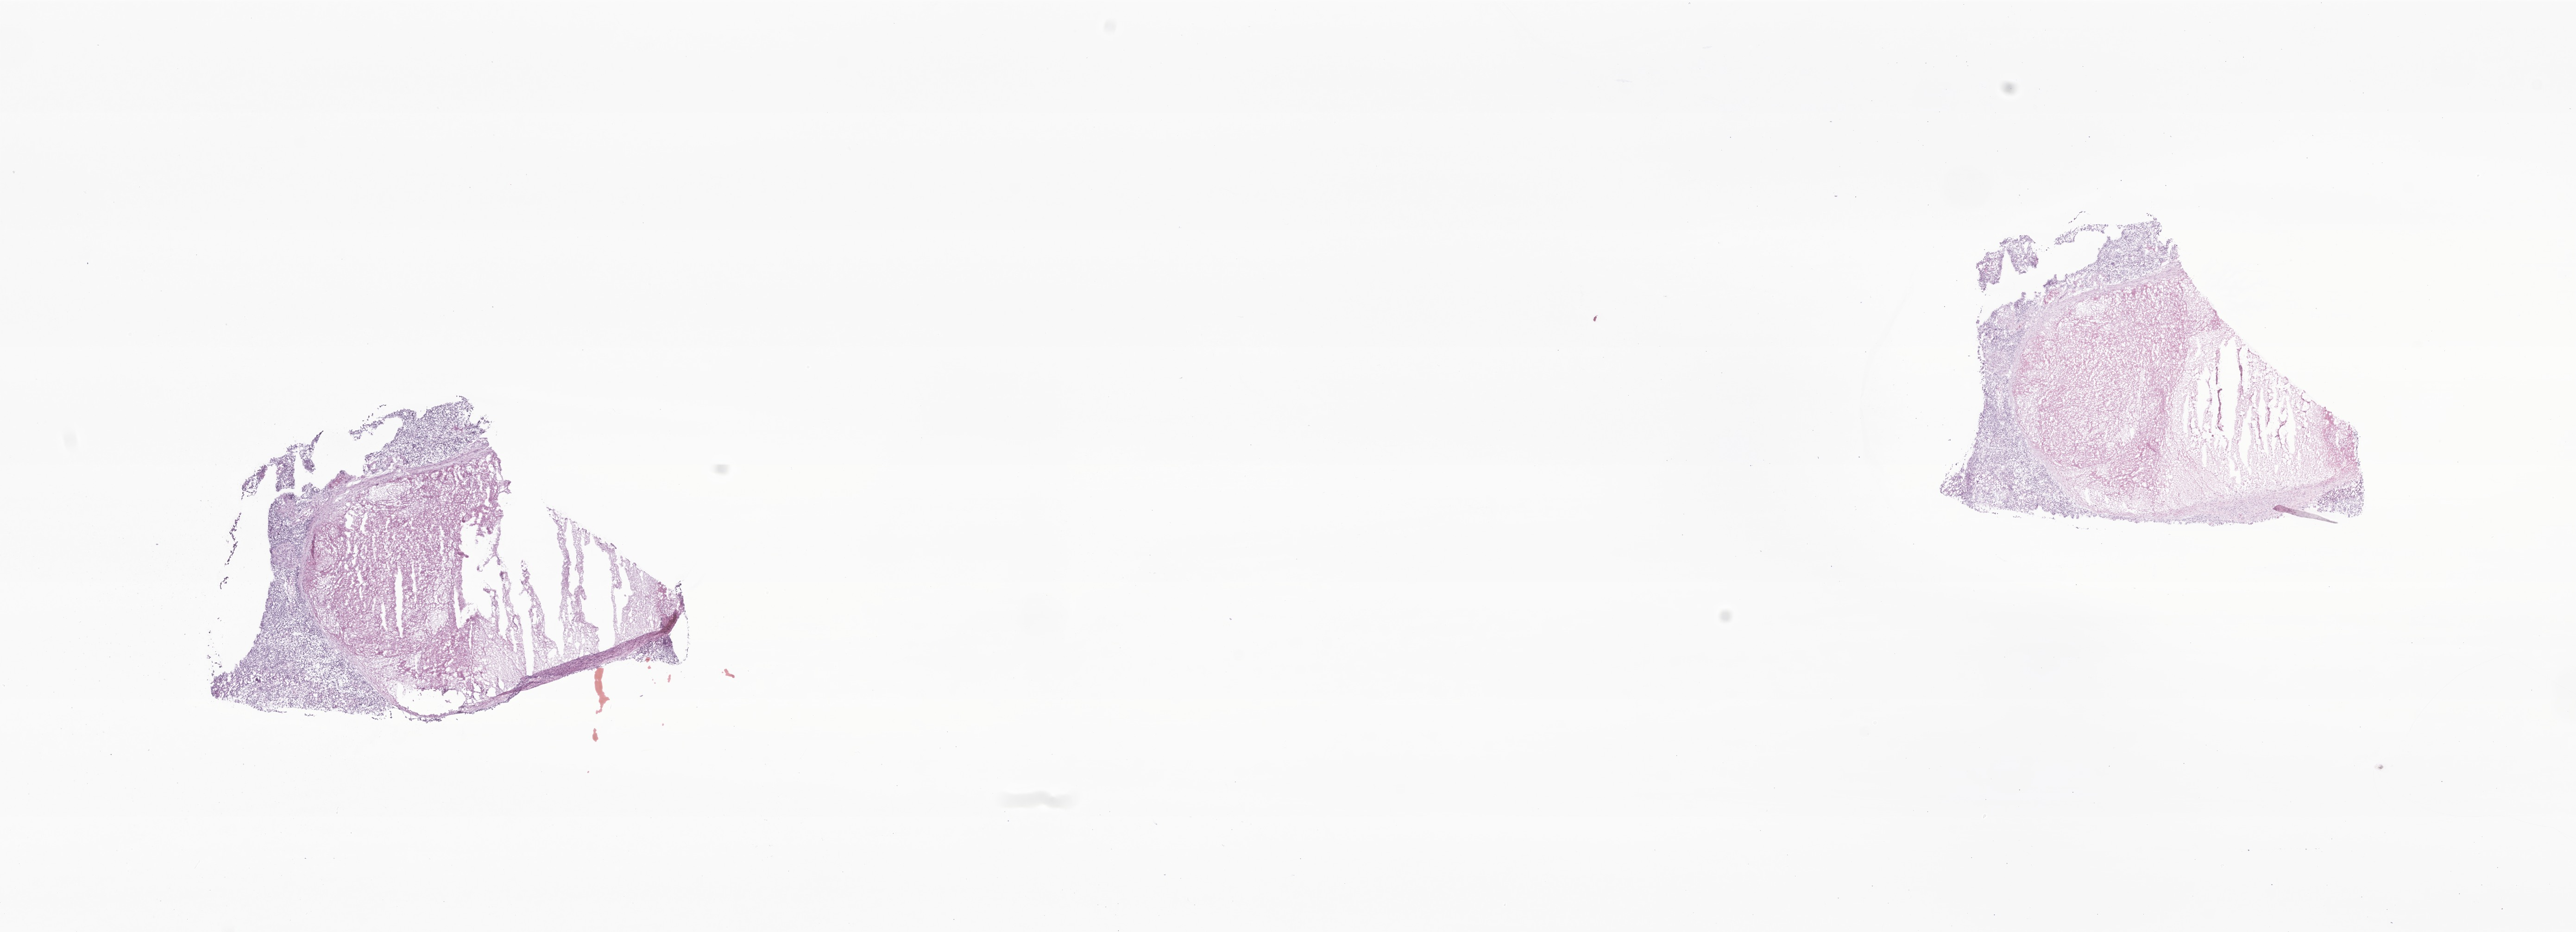
Digitized H&E-stained section of tumor tissue from the cerebrum, a low-resolution overview of the entire scanned area, about 23.4 x 8.5 mm, cryosection (OCT / tissue freezing medium). Patient male; age 356 days.
Recorded diagnosis: Neoplasm, uncertain whether benign or malignant.